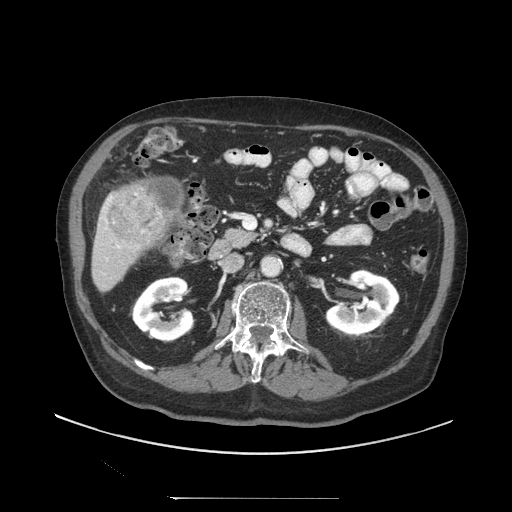
Contrast-enhanced abdominal CT (liver protocol), one axial slice; position 35 of 97 along the scan axis; reconstruction kernel STANDARD; 140 kVp; soft-tissue window (W 400 / L 40 HU); 2.5 mm slice thickness; 512 × 512 image matrix, field of view 450 × 450 mm. From the clinical record (not read from this slice): diagnosis: hepatocellular carcinoma (patient treated with transarterial chemoembolisation; whether this scan precedes or follows treatment is not stated here); TNM stage (as recorded): Stage-IIIC; Child-Pugh class: A; tumour differentiation: well differentiated; tumour nodularity: uninodular.
Structures marked on this image (semi-automatically segmented with operator editing):
- liver parenchyma outside the tumour (the mass and vessels are separate outlines, so this box may not span the whole liver): box from (x=92, y=182) to (x=172, y=292) px
- mass: (x=108, y=186)–(x=166, y=244)
- liver vessels: (x=102, y=196)–(x=121, y=249)